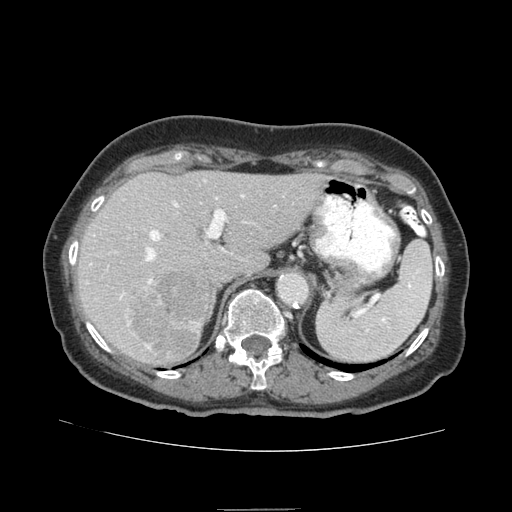
Contrast-enhanced abdominal CT (liver protocol), one axial slice; position 54 of 95 along the scan axis; reconstruction kernel STANDARD; 140 kVp; soft-tissue window (W 400 / L 40 HU); 2.5 mm slice thickness; 512 × 512 image matrix. From the clinical record (not read from this slice): diagnosis: hepatocellular carcinoma (patient treated with transarterial chemoembolisation; whether this scan precedes or follows treatment is not stated here); TNM stage (as recorded): Stage-IVA; Child-Pugh class: B.
Annotated regions visible in this slice (semi-automatic segmentation, software-assisted and operator-edited):
- liver parenchyma outside the tumour (the mass and vessels are separate outlines, so this box may not span the whole liver): bounding box <76,170,327,364> (left, top, right, bottom; pixels)
- mass: <128,272,213,357>
- liver vessels: <120,195,244,349>